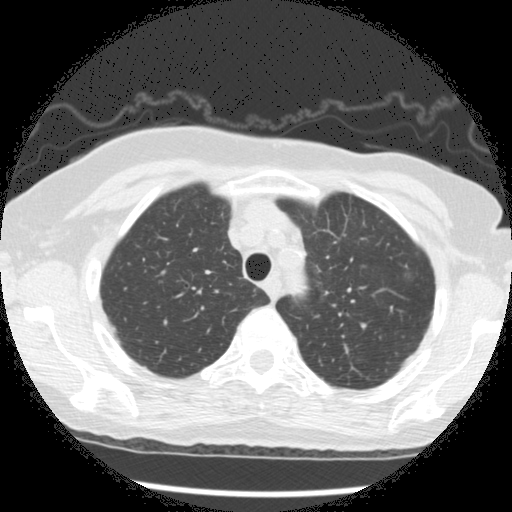
Axial slice from a low-dose chest CT screening exam; second screening round (one year after baseline); lung window (W 1500 / L -600 HU); 2.5 mm slice thickness; 120 kVp; slice 41 of 266 in the series; 512 × 512 image matrix, field of view 320 × 320 mm. Female participant, aged 73 years at enrolment. Former smoker at enrolment.
Expert reader's lesion annotation, bounding box <392,243,434,285> (left, top, right, bottom; pixels). The screening reader recorded 3 non-calcified nodules or masses ≥4 mm on this exam (left upper lobe, left upper lobe, left upper lobe); which of them this box marks is not recorded. Official screen result: positive, change unspecified: nodule(s) >= 4 mm or enlarging nodule(s), mass(es), or other non-specific abnormalities suspicious for lung cancer.